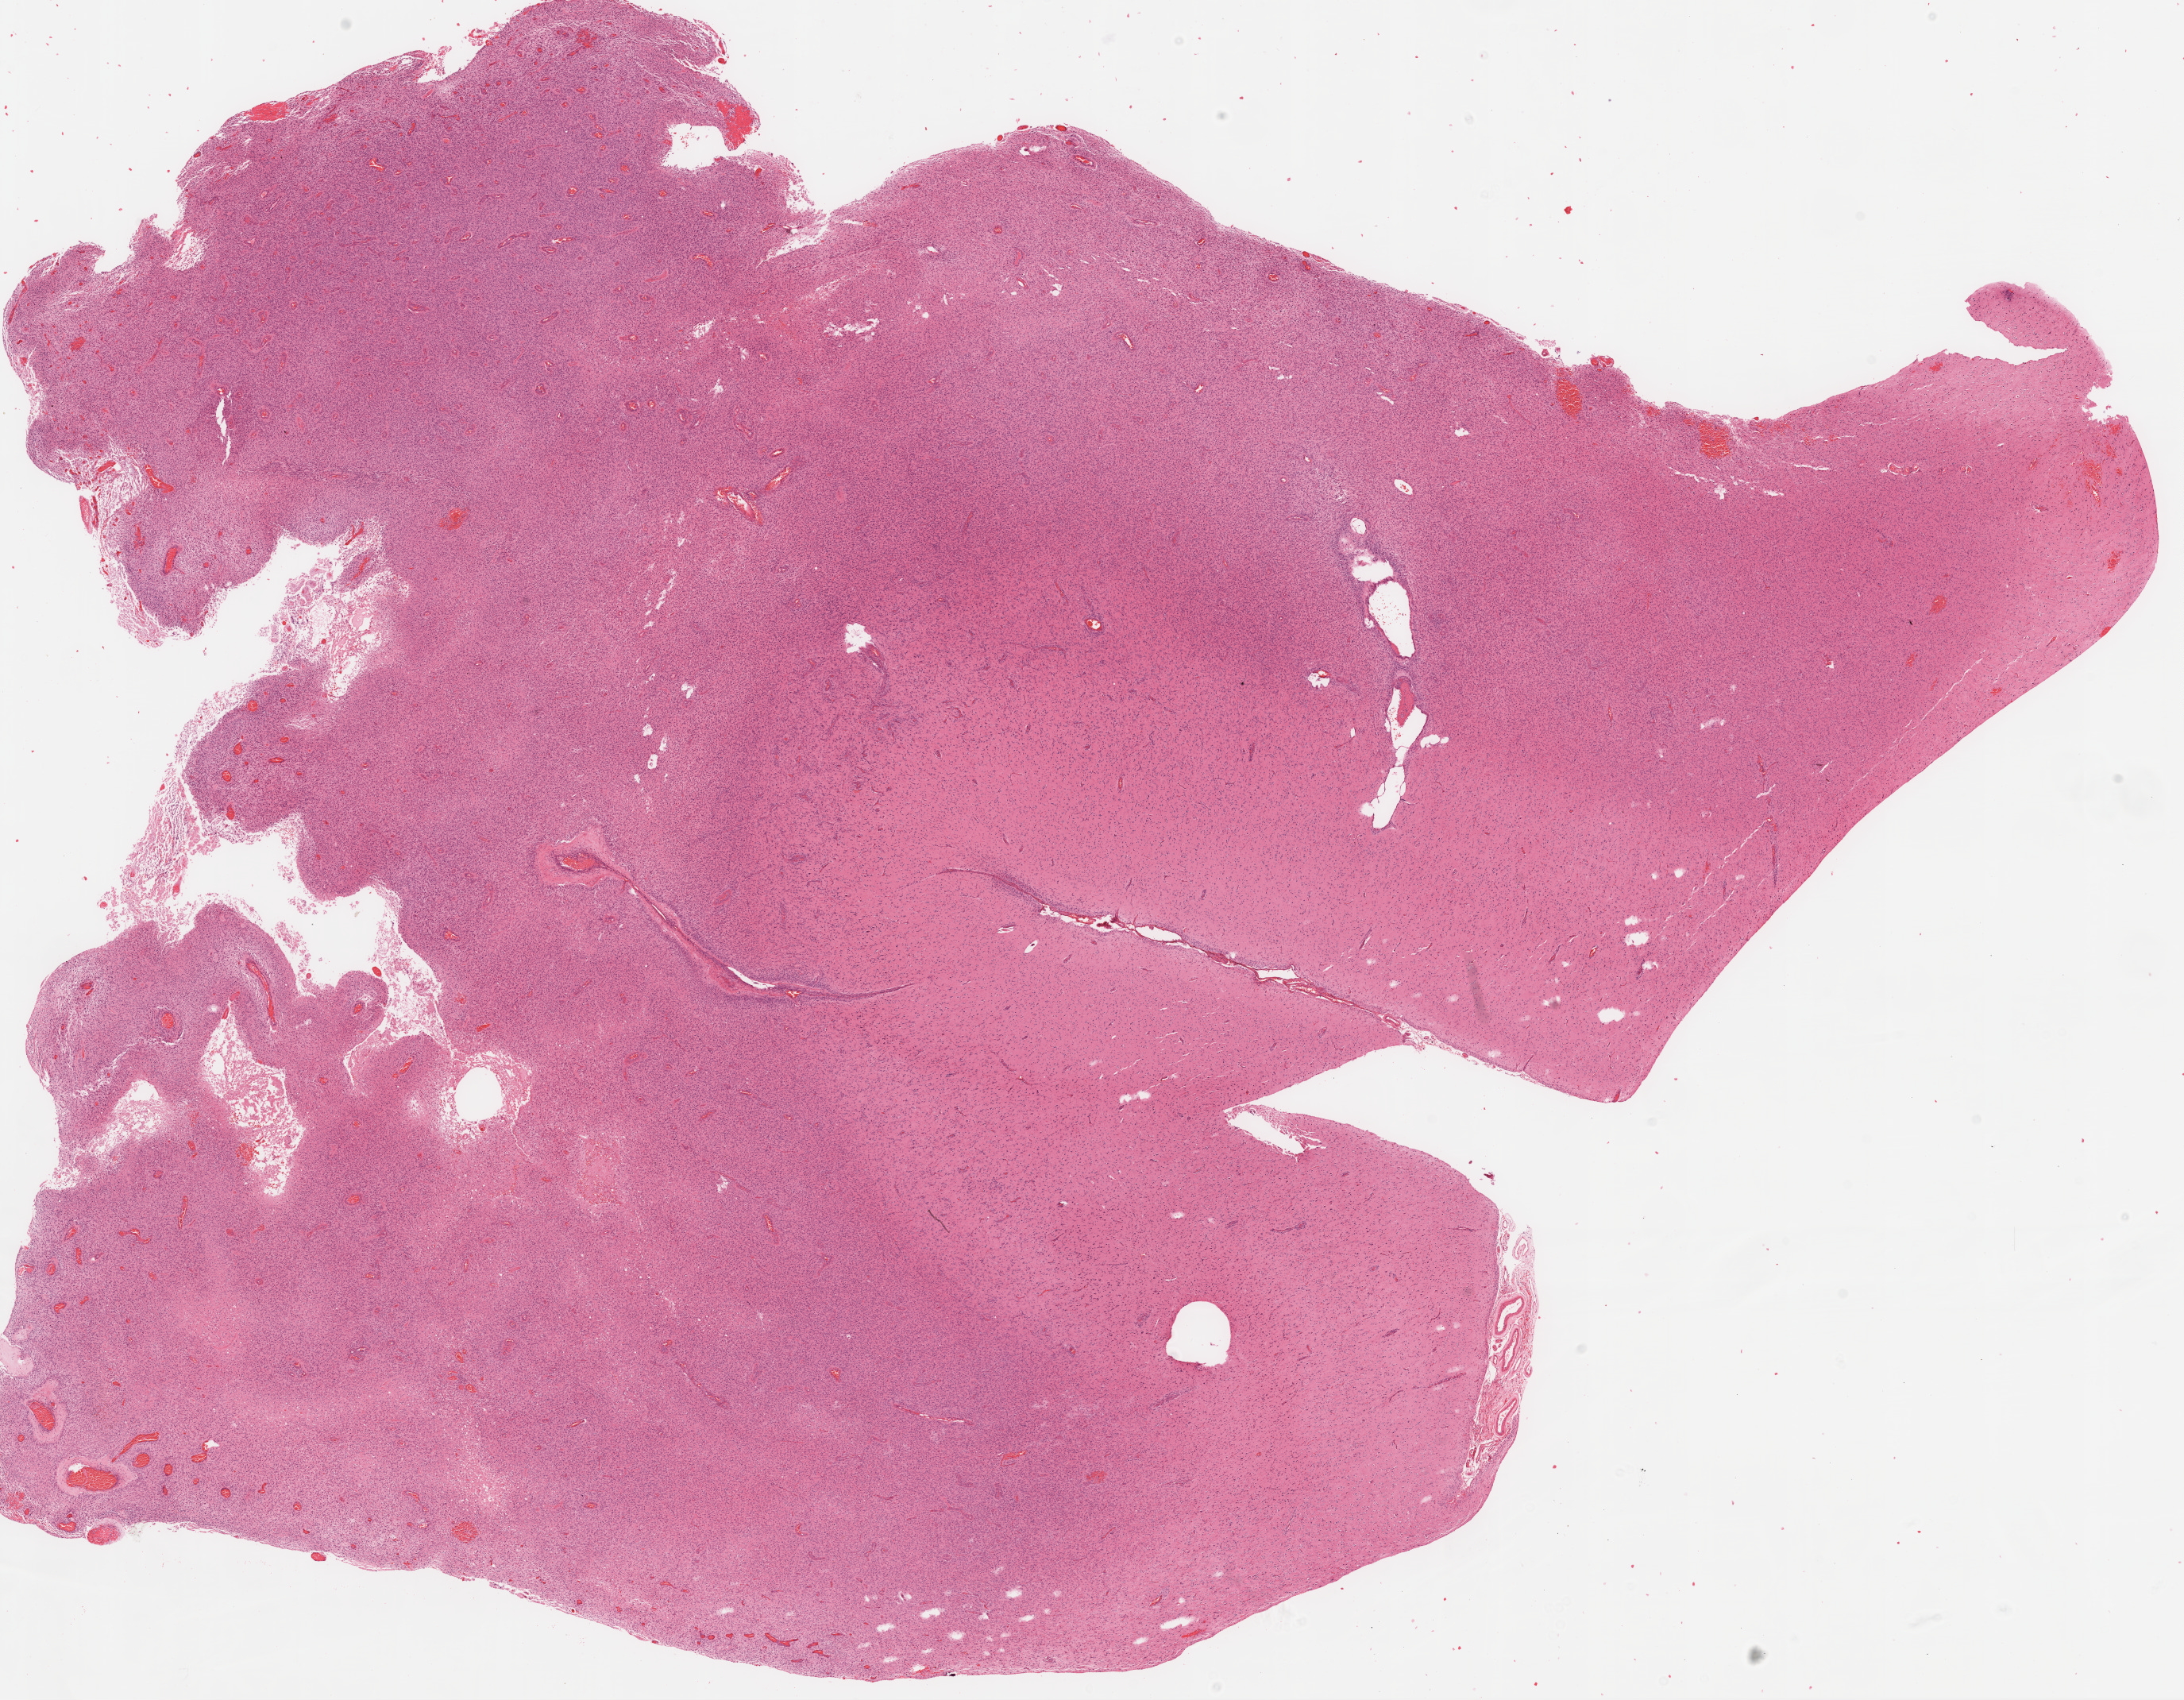
H&E-stained whole-slide image — a low-resolution overview of the entire scanned area, about 22.1 x 17.2 mm (acquisition: 20x scan); formalin-fixed paraffin-embedded (FFPE) diagnostic section; brain, primary tumour sample. Female patient; age at initial diagnosis 74 years.
Diagnosis: Glioblastoma.